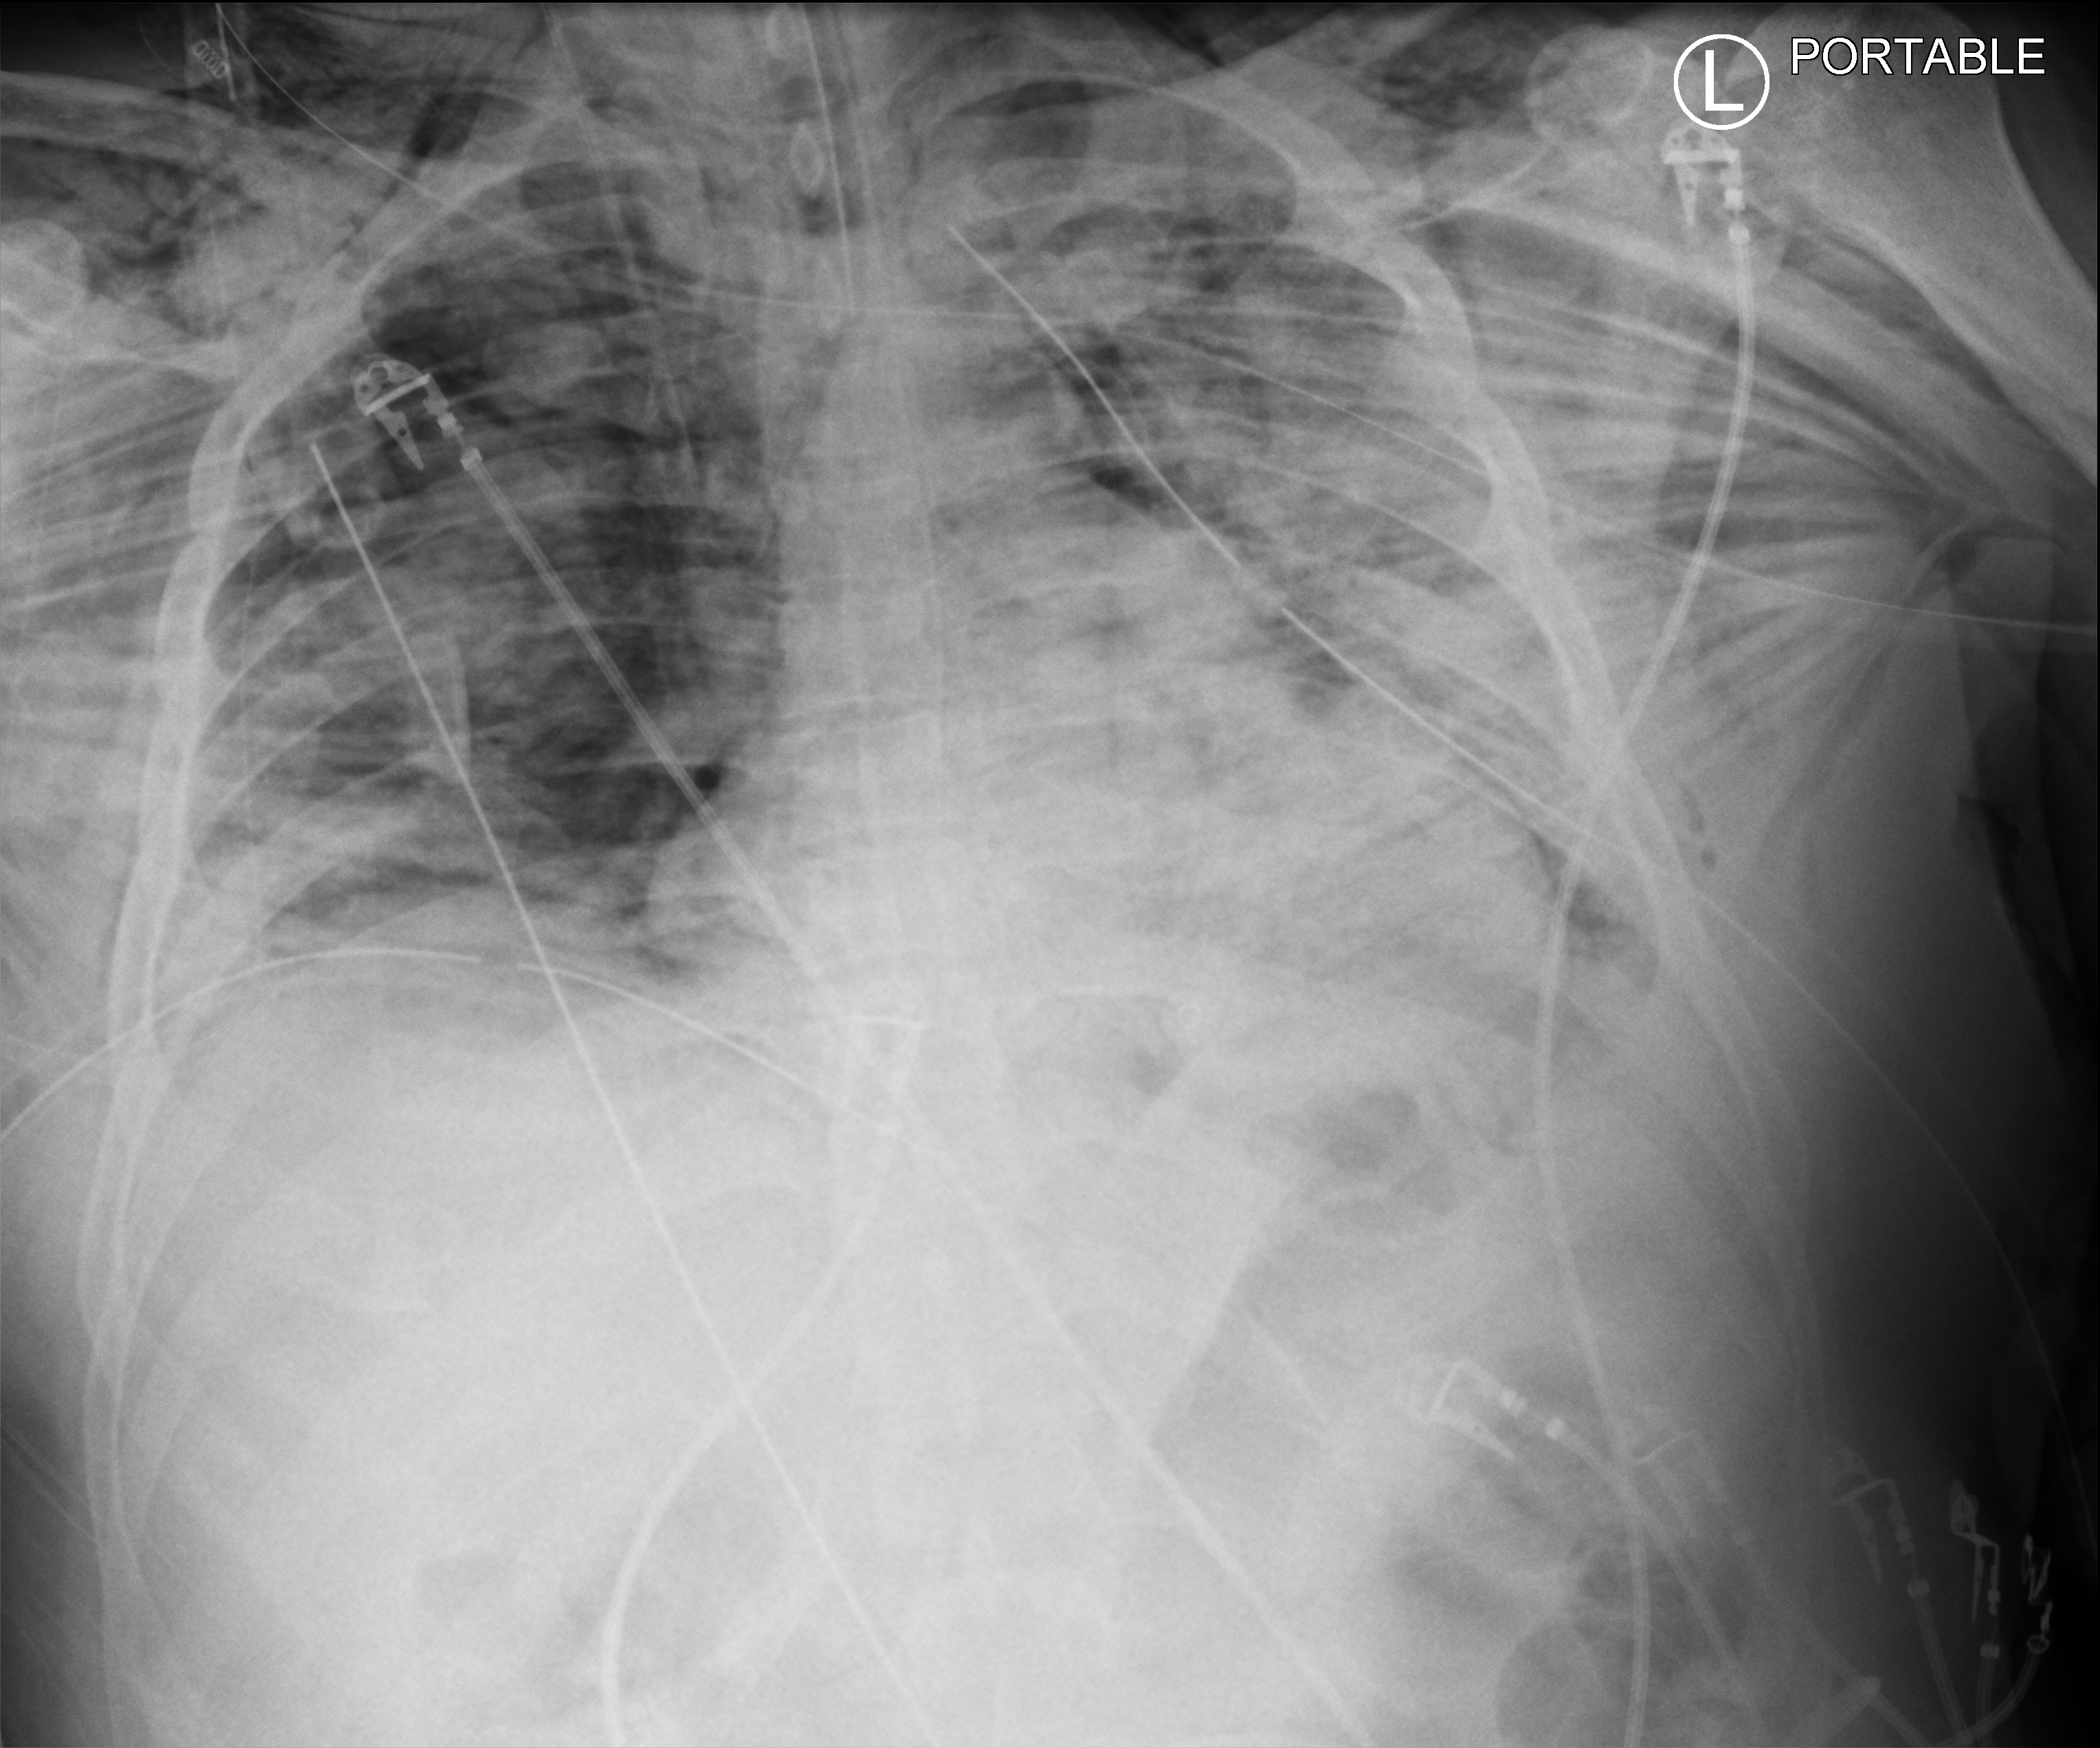
Chest X-ray (portable); anteroposterior (AP) projection. Patient hospitalised with COVID-19; male, aged 18–59 years.
Admission-level facts for this patient (not findings on this image; timing relative to this image not recorded): mechanically ventilated during this hospital stay: yes.